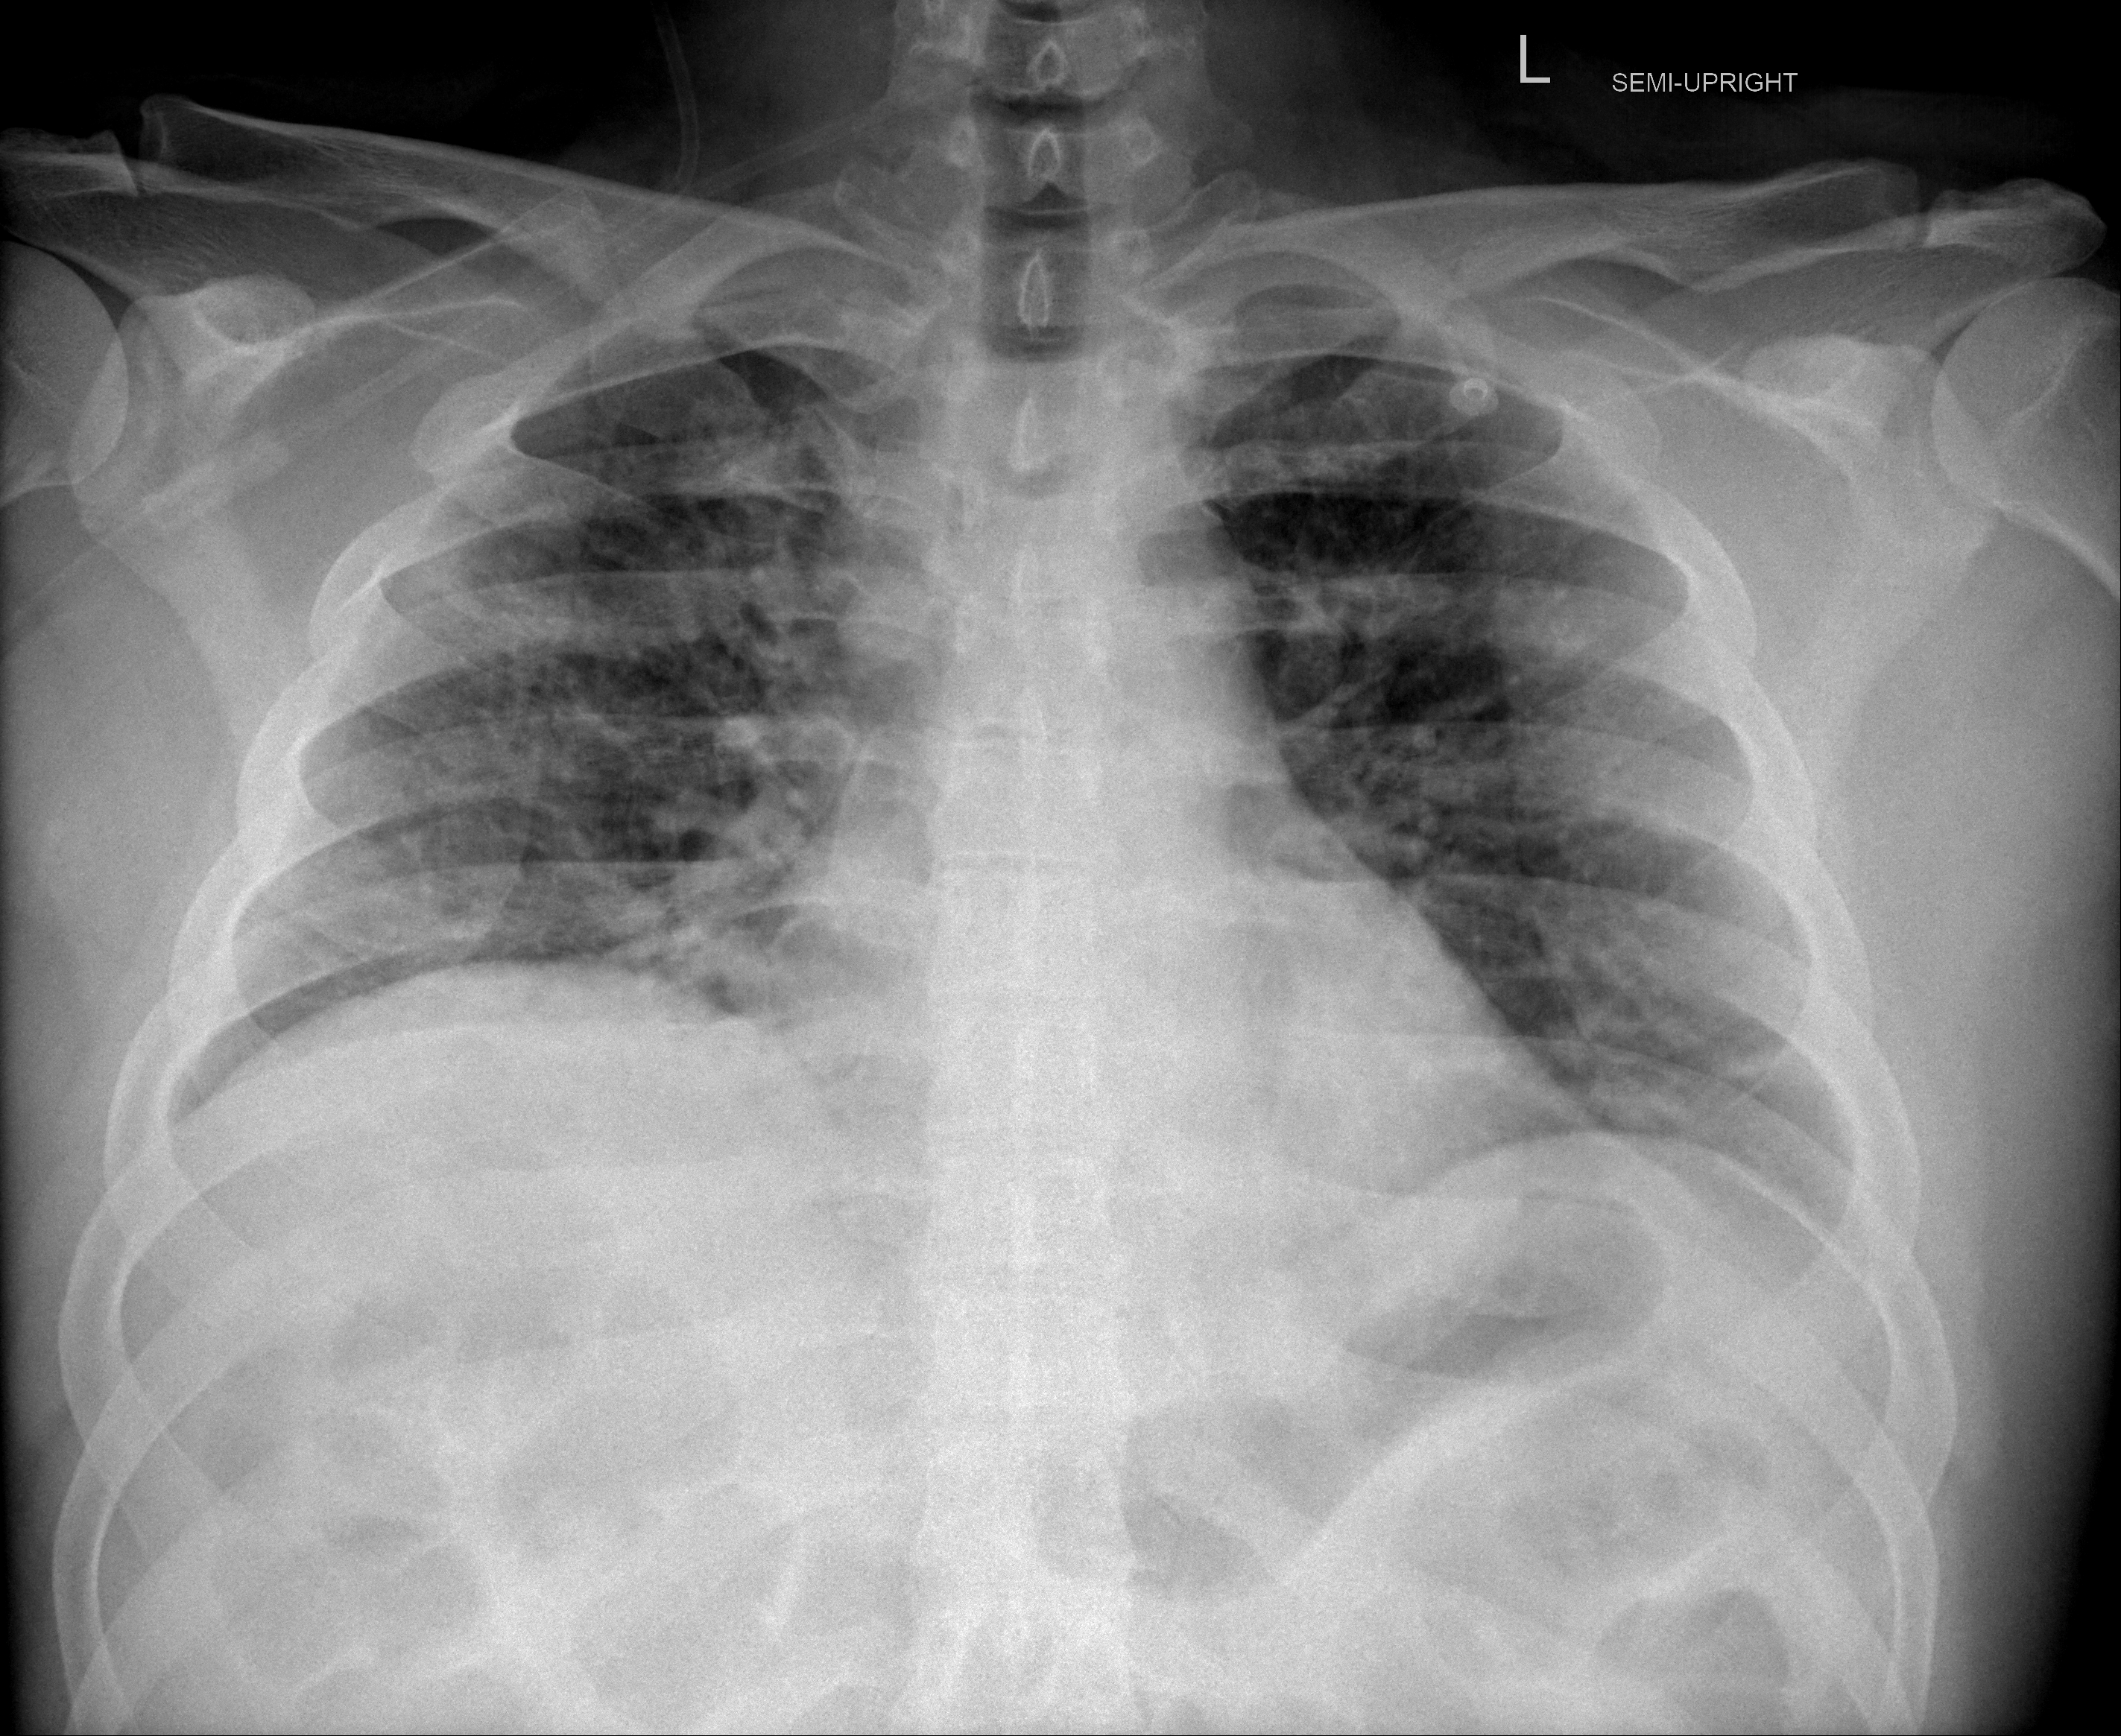
Portable chest radiograph, AP projection. Male patient, age 38 years; imaged 3 days after the COVID-19 diagnosis.
Radiologist key findings (as recorded): mild bibasilar atelectasis, patchy lung opacities bilaterally have not changed significantly.